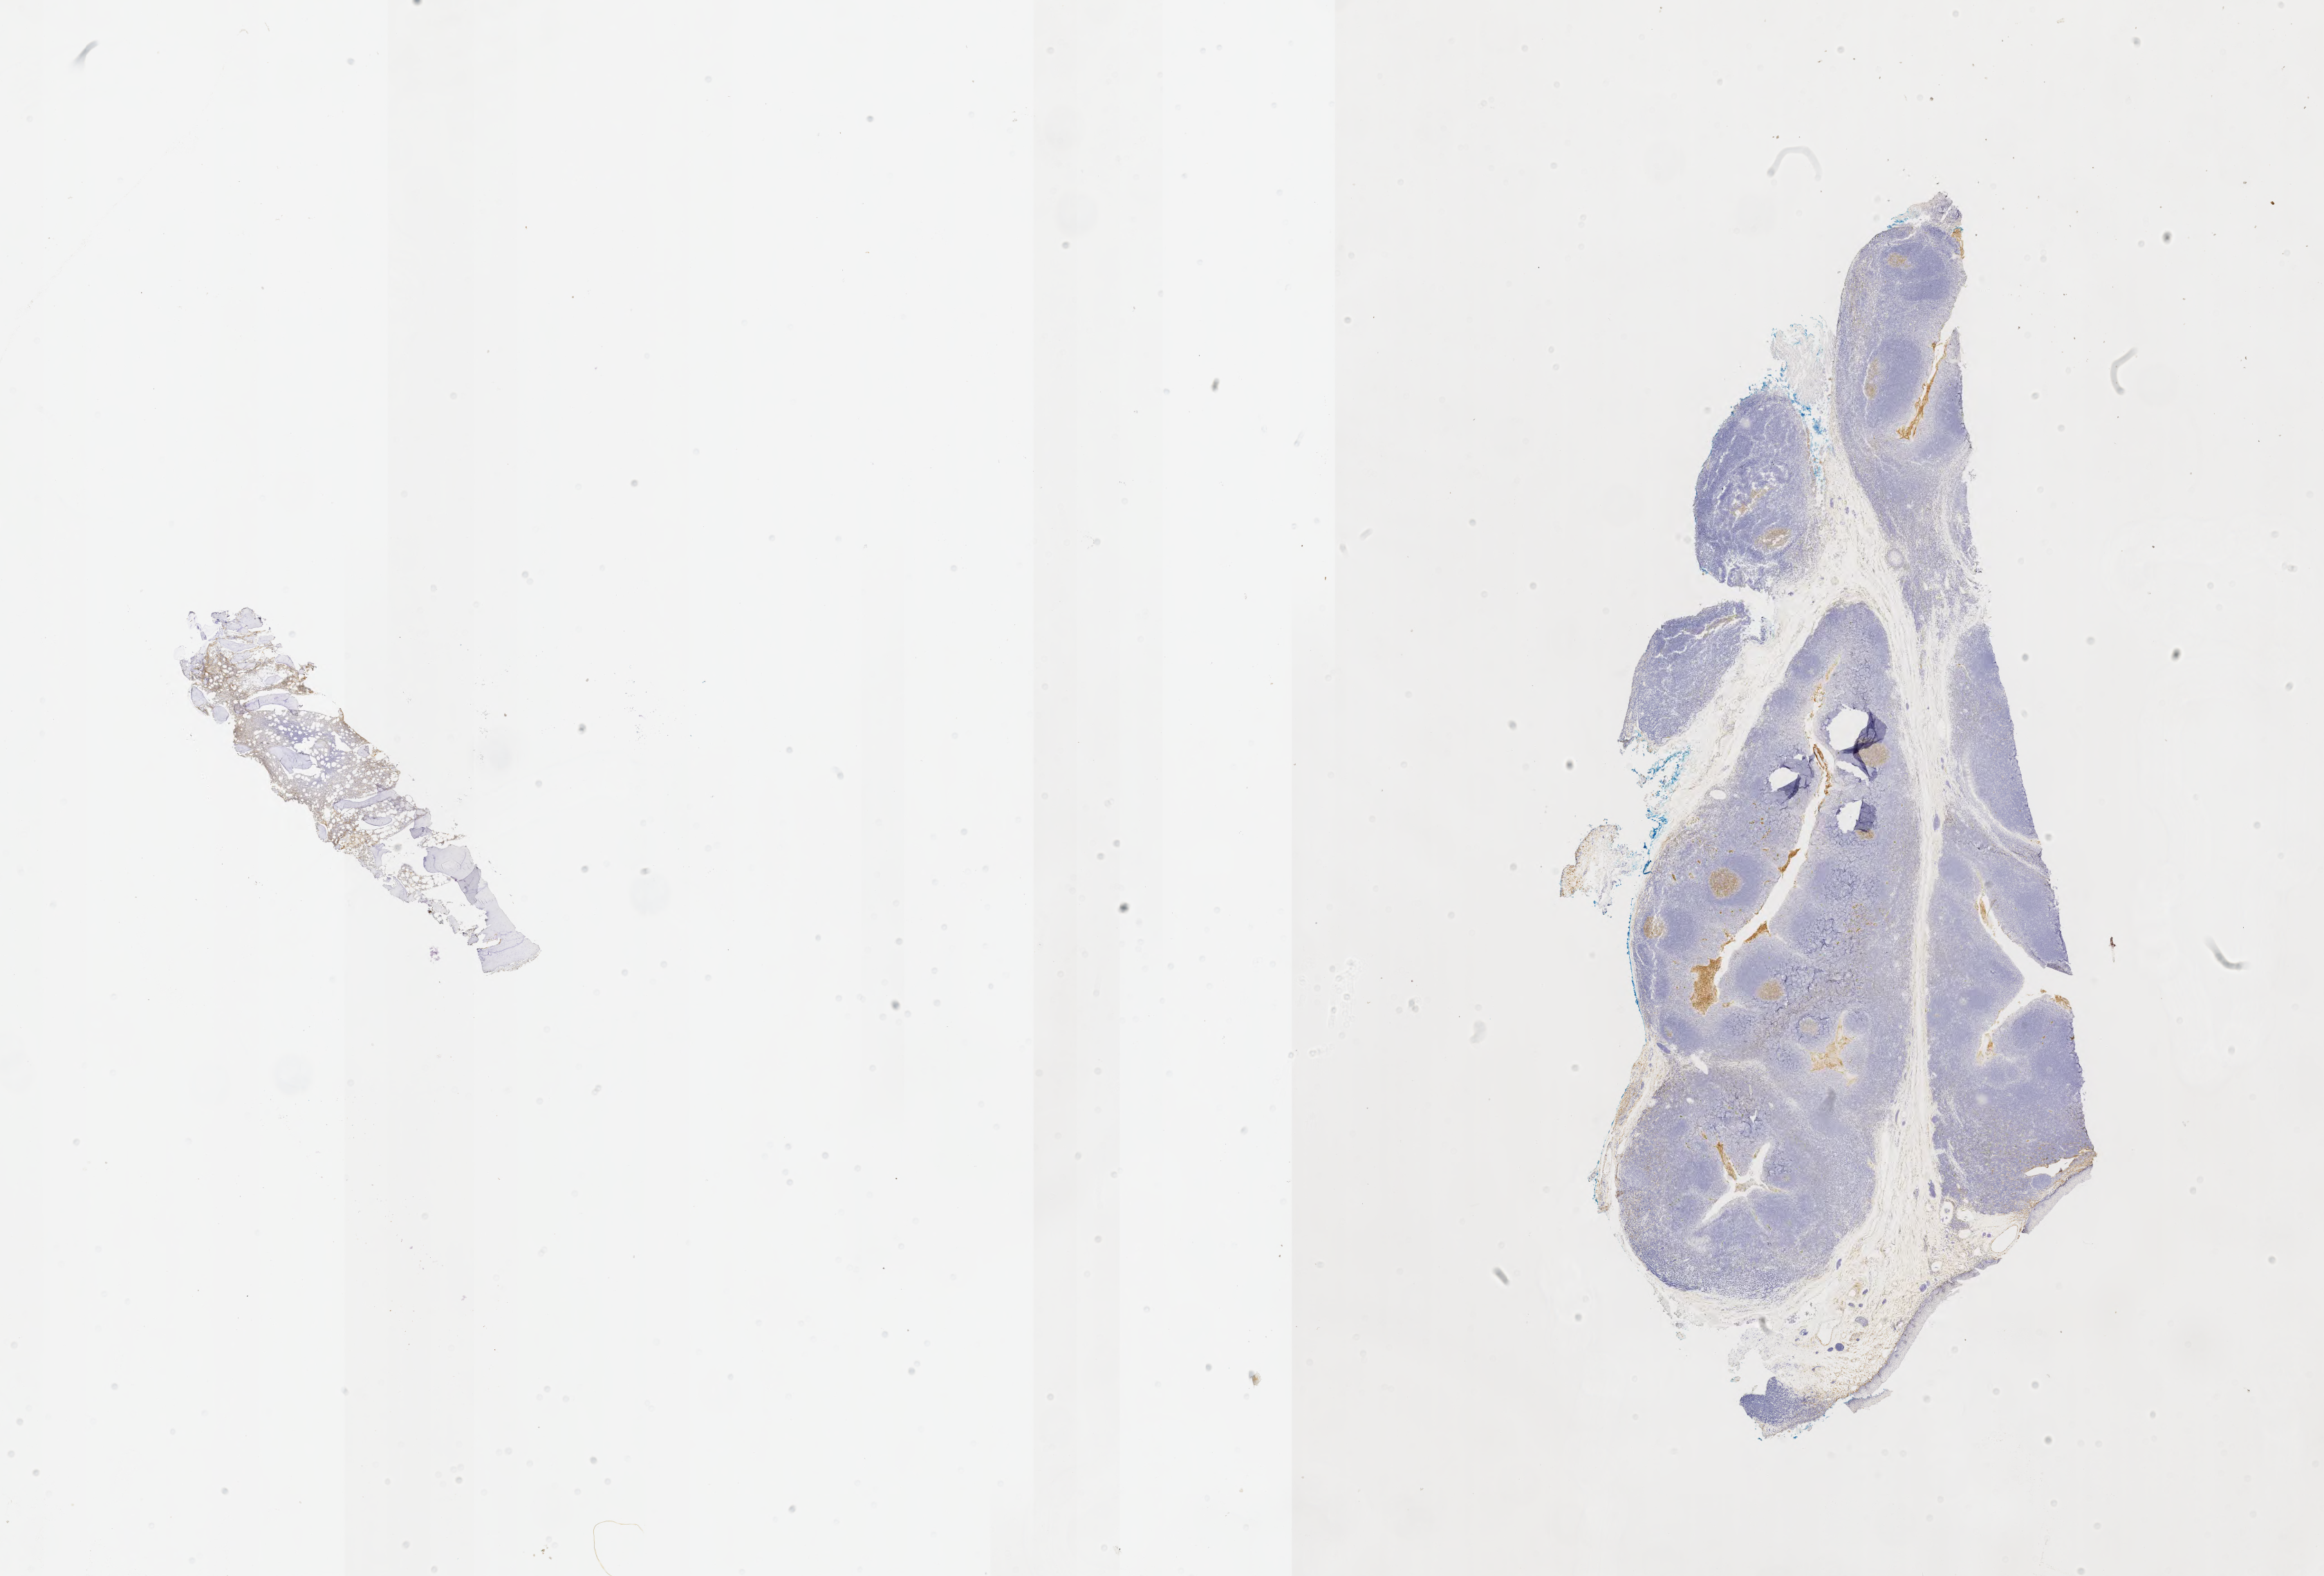
Immunohistochemistry (IHC) whole-slide image stained for CD10, low-resolution overview of the scanned area, about 27.2 x 18.4 mm. Tumor tissue. Site: bone marrow. Female, age 4 years at initial diagnosis.
Diagnosis: Burkitt lymphoma, NOS.